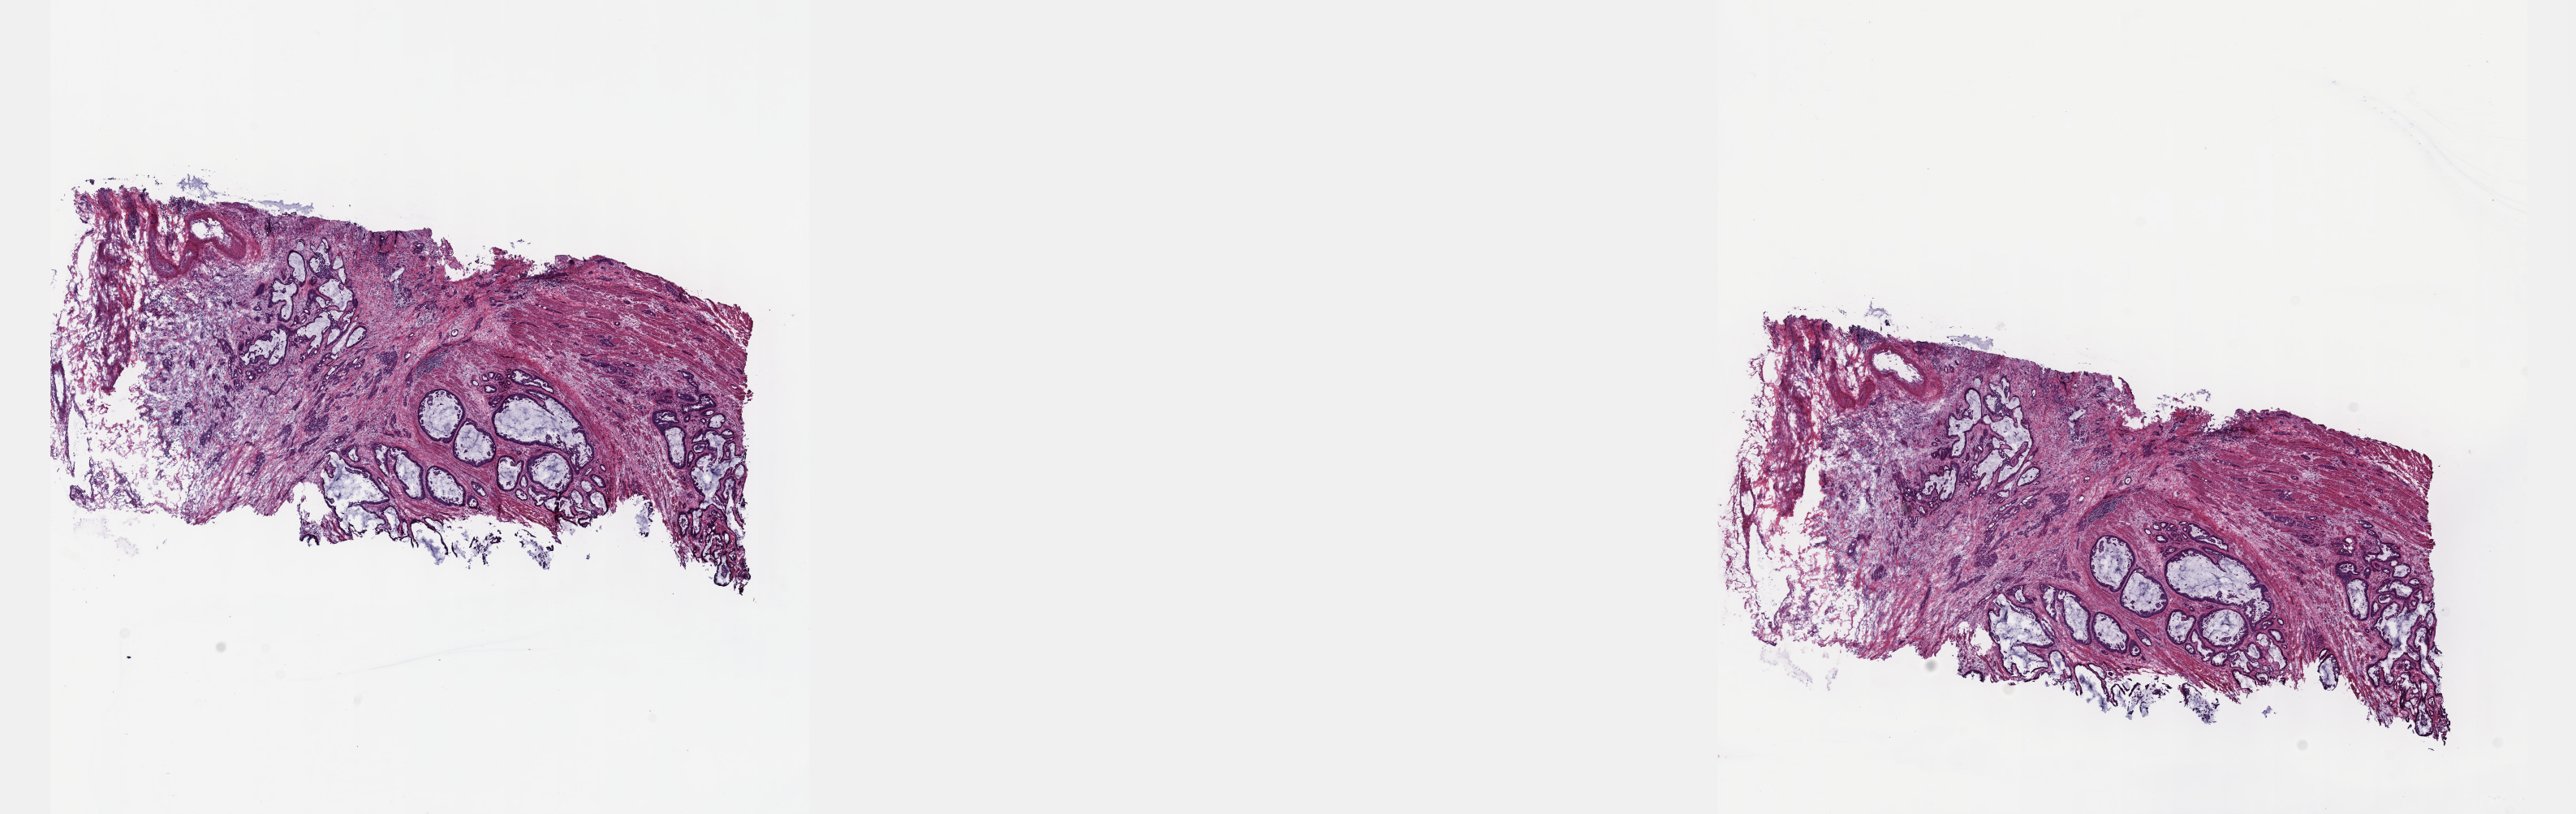
Whole-slide histology image, H&E, shown as a low-resolution overview of the whole scanned area (about 25.7 x 8.1 mm, slide scanned at 40x); frozen section; esophagus, primary tumour sample. Patient: male, age at initial diagnosis 69 years. Histologic grade: GX (grade cannot be assessed). Pathologist review of this section (percent, as recorded): tumour cells 100%, tumour nuclei 60%, normal cells 0%, stromal cells 0%, necrosis 0%. Infiltration values recorded for this section: lymphocyte infiltration 5%, monocyte infiltration 0%, neutrophil infiltration 0%.
Histologic diagnosis: Adenocarcinoma, NOS (lower third of esophagus). AJCC pathologic stage: IIB (5th edition).